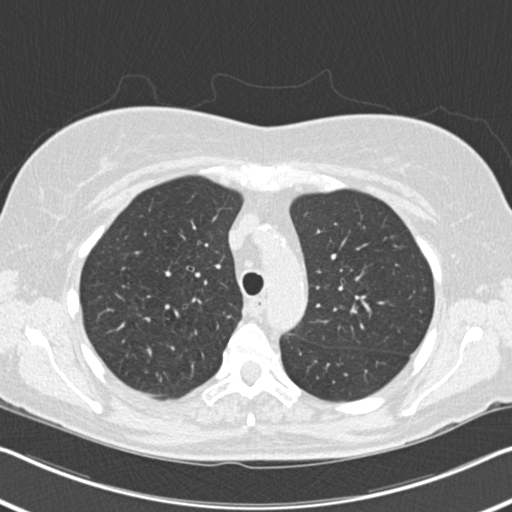
Axial slice from a low-dose chest CT screening exam. Second screening round (one year after baseline). Lung window (W 1500 / L -600 HU). 2 mm slice thickness. Standard (soft-tissue) reconstruction kernel (B30f). 512 × 512 image matrix. Female, age 60 years at enrolment.
- Expert-annotated lung lesion, box from (x=384, y=231) to (x=426, y=267) px.
- The screening reader recorded 6 non-calcified nodules or masses ≥4 mm on this exam (right upper lobe, right middle lobe, right lower lobe, right lower lobe, left lower lobe, lingula); which of them this box marks is not recorded.
- Lung cancer was diagnosed 495 days after this screen (after the third annual screen): non-small cell carcinoma, left upper lobe, poorly differentiated (G3), stage IB (AJCC 6th edition), 7 mm at pathology.